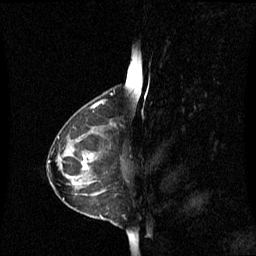
Breast MRI (dynamic contrast-enhanced), one sagittal slice; position 37 of 60 along the scan axis; dynamic contrast-enhanced series, image 2 of 3 at this slice position (ordered by acquisition); 1.5 T; TE 4.2 ms, TR 8.4 ms; 2.1 mm slice thickness; 256 × 256 image matrix, field of view 240 × 240 mm. Patient: female, 42 years. Case-level facts recorded for this patient, not image findings: setting: breast cancer imaged before/during neoadjuvant chemotherapy; receptor status: HR-positive, HER2-negative.
Outlined on this slice (semi-automatically segmented with operator editing):
- analysis volume of interest (the breast-tissue region the enhancement analysis was run in; not a lesion): bounding box (x1, y1, x2, y2) in pixels: (60, 124, 112, 195)
- tumour enhancement mask (voxels above the 70 % enhancement threshold inside the analysis volume of interest): (81, 156, 92, 169)